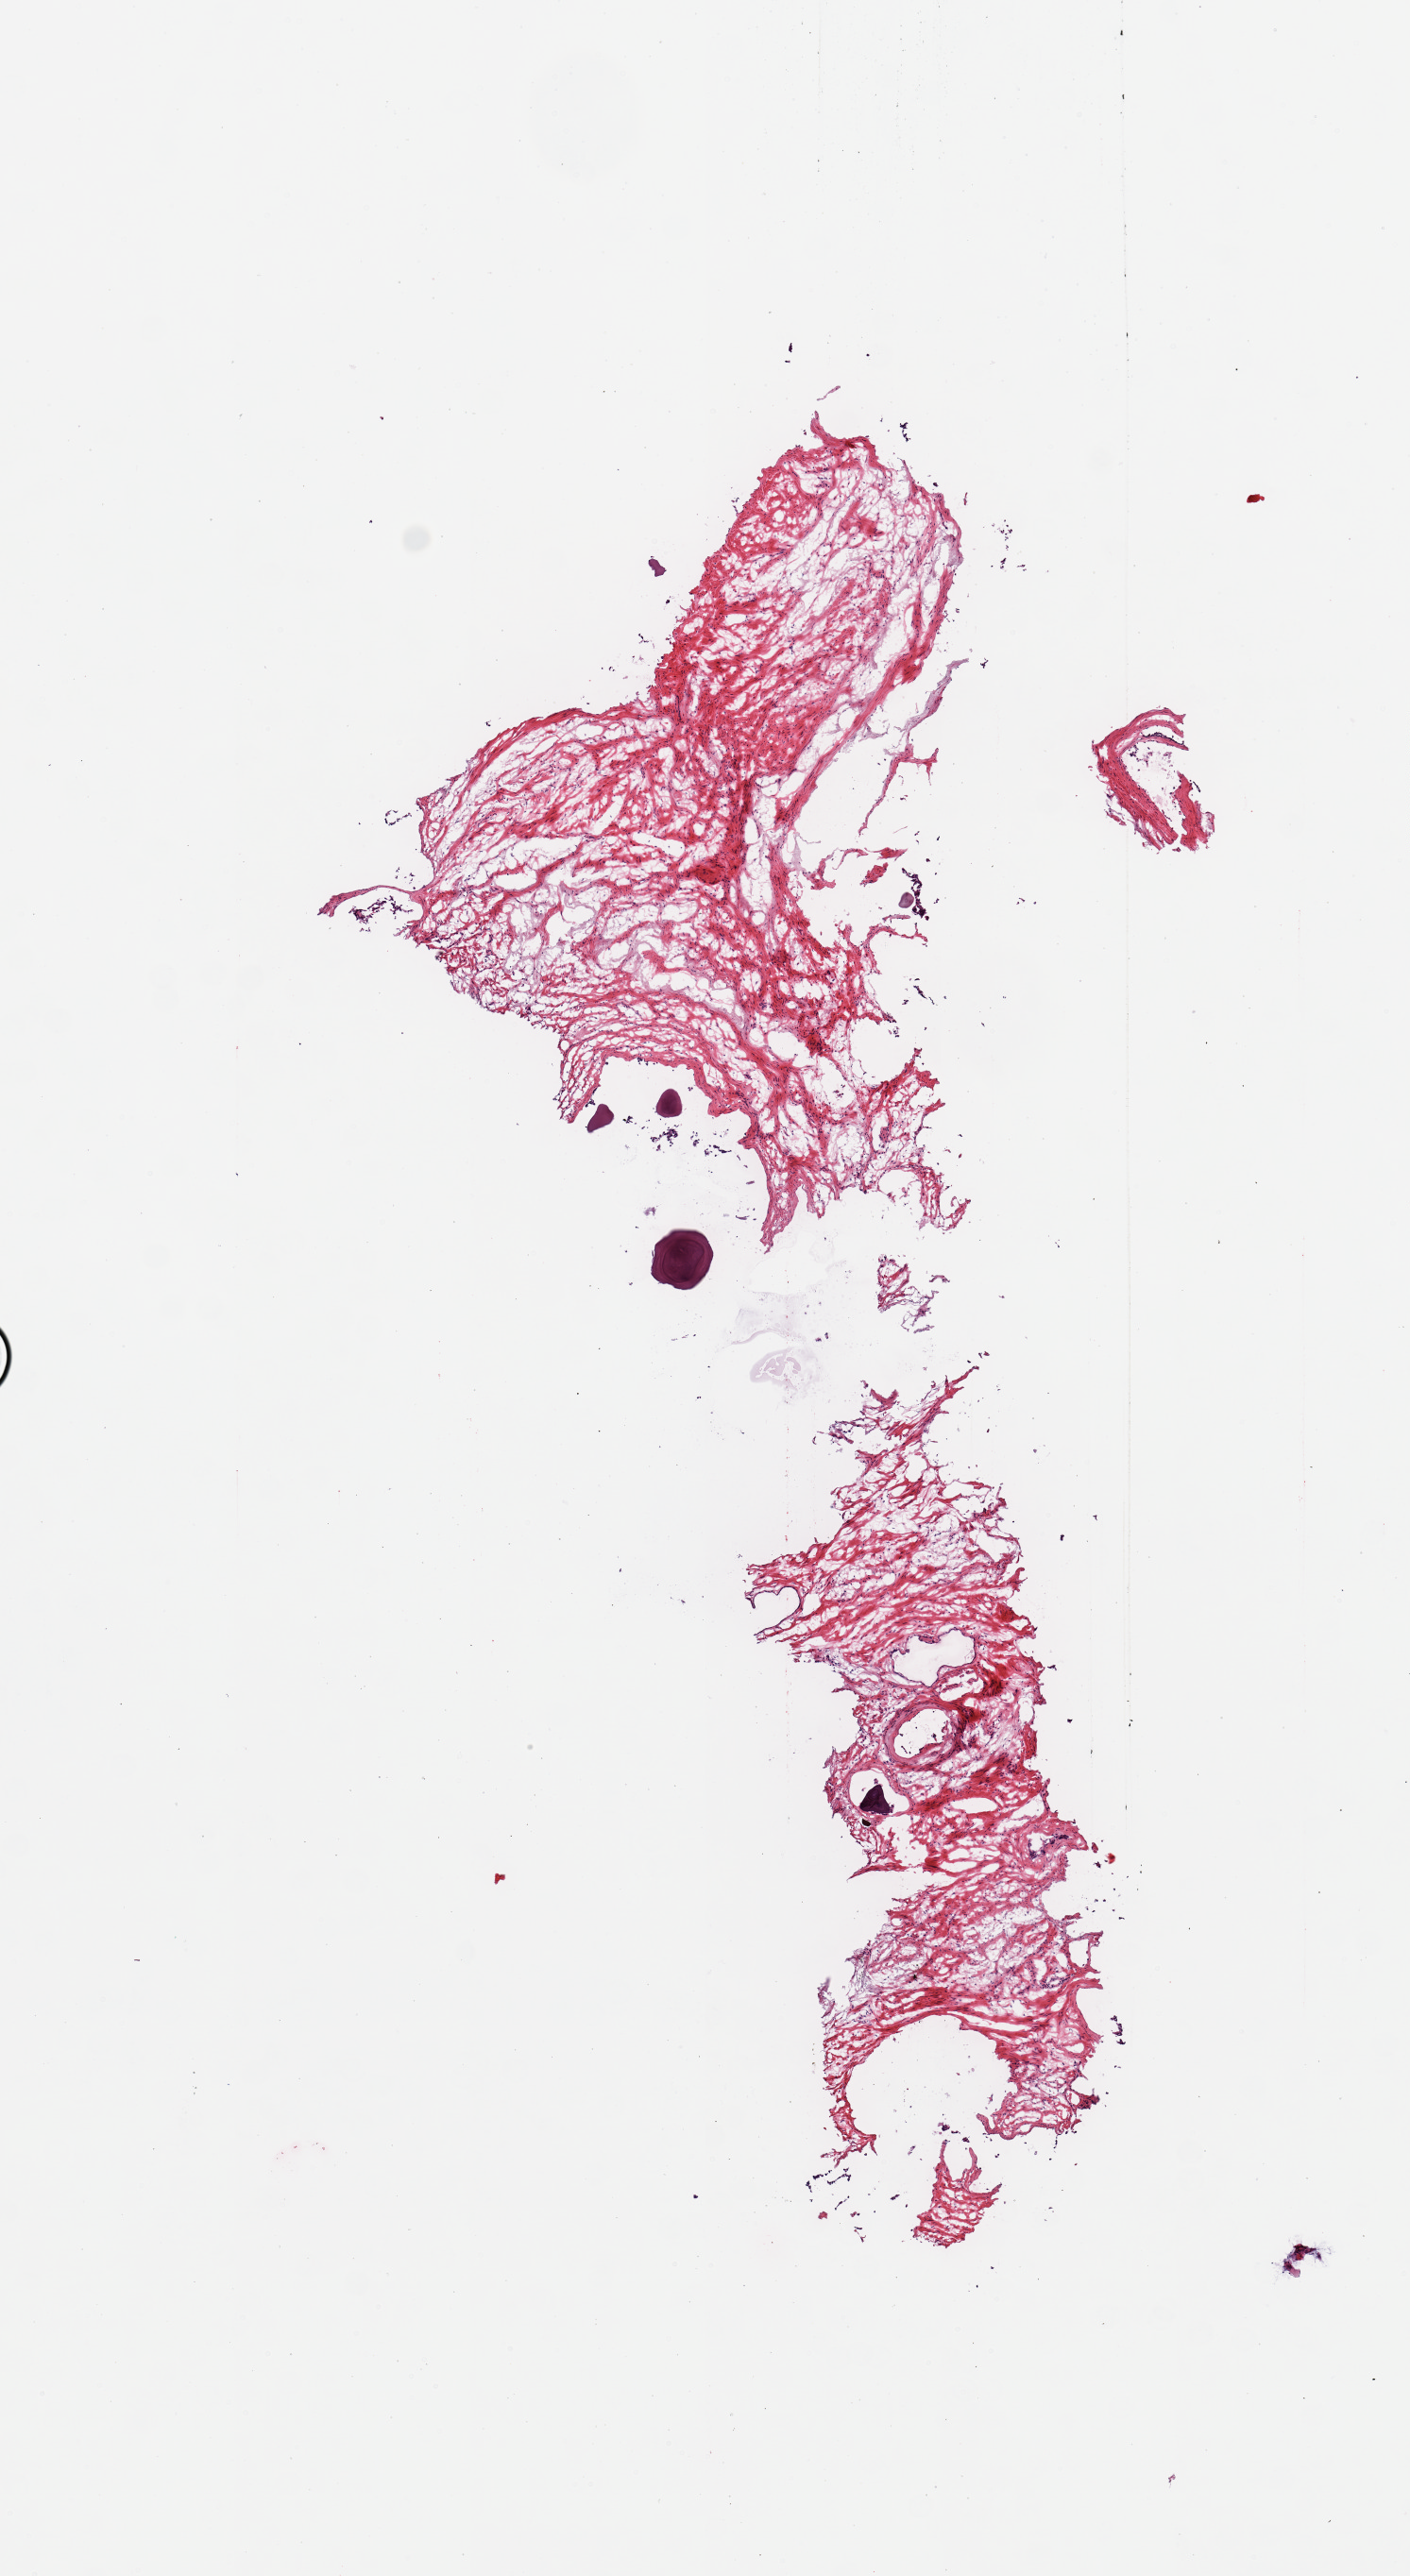
H&E whole-slide image — whole scanned area (about 5.9 x 10.8 mm) shown as a low-resolution overview. Donor: male.
* specimen: frozen section; sampled site (target tissue): prostate; tissue donor sample